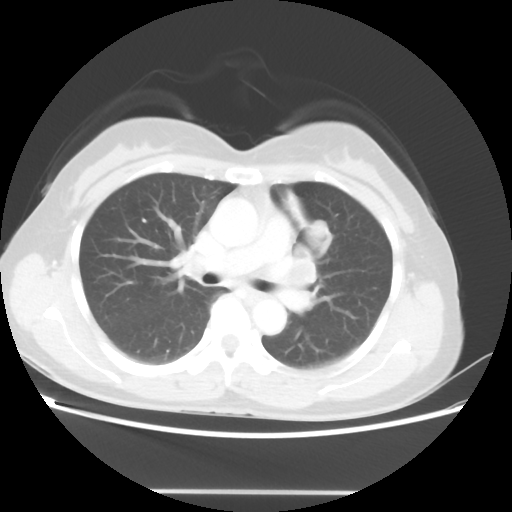
Chest CT, one axial slice. Slice 28 of 46 in the series (ordered by position). Reconstruction kernel STANDARD. 100 kVp. Lung window (W 1500 / L -600 HU). 5 mm slice thickness. 512 × 512 image matrix, field of view 360 × 360 mm. Patient: female, 50 years. From the clinical record (not read from this slice): clinical TNM (as recorded): T1c N1 M0; histopathological grade: G3.
Annotated regions visible in this slice (bounding box drawn by a radiologist):
- lung tumour (recorded histology: adenocarcinoma): bounding box (x1, y1, x2, y2) in pixels: (311, 221, 333, 249)